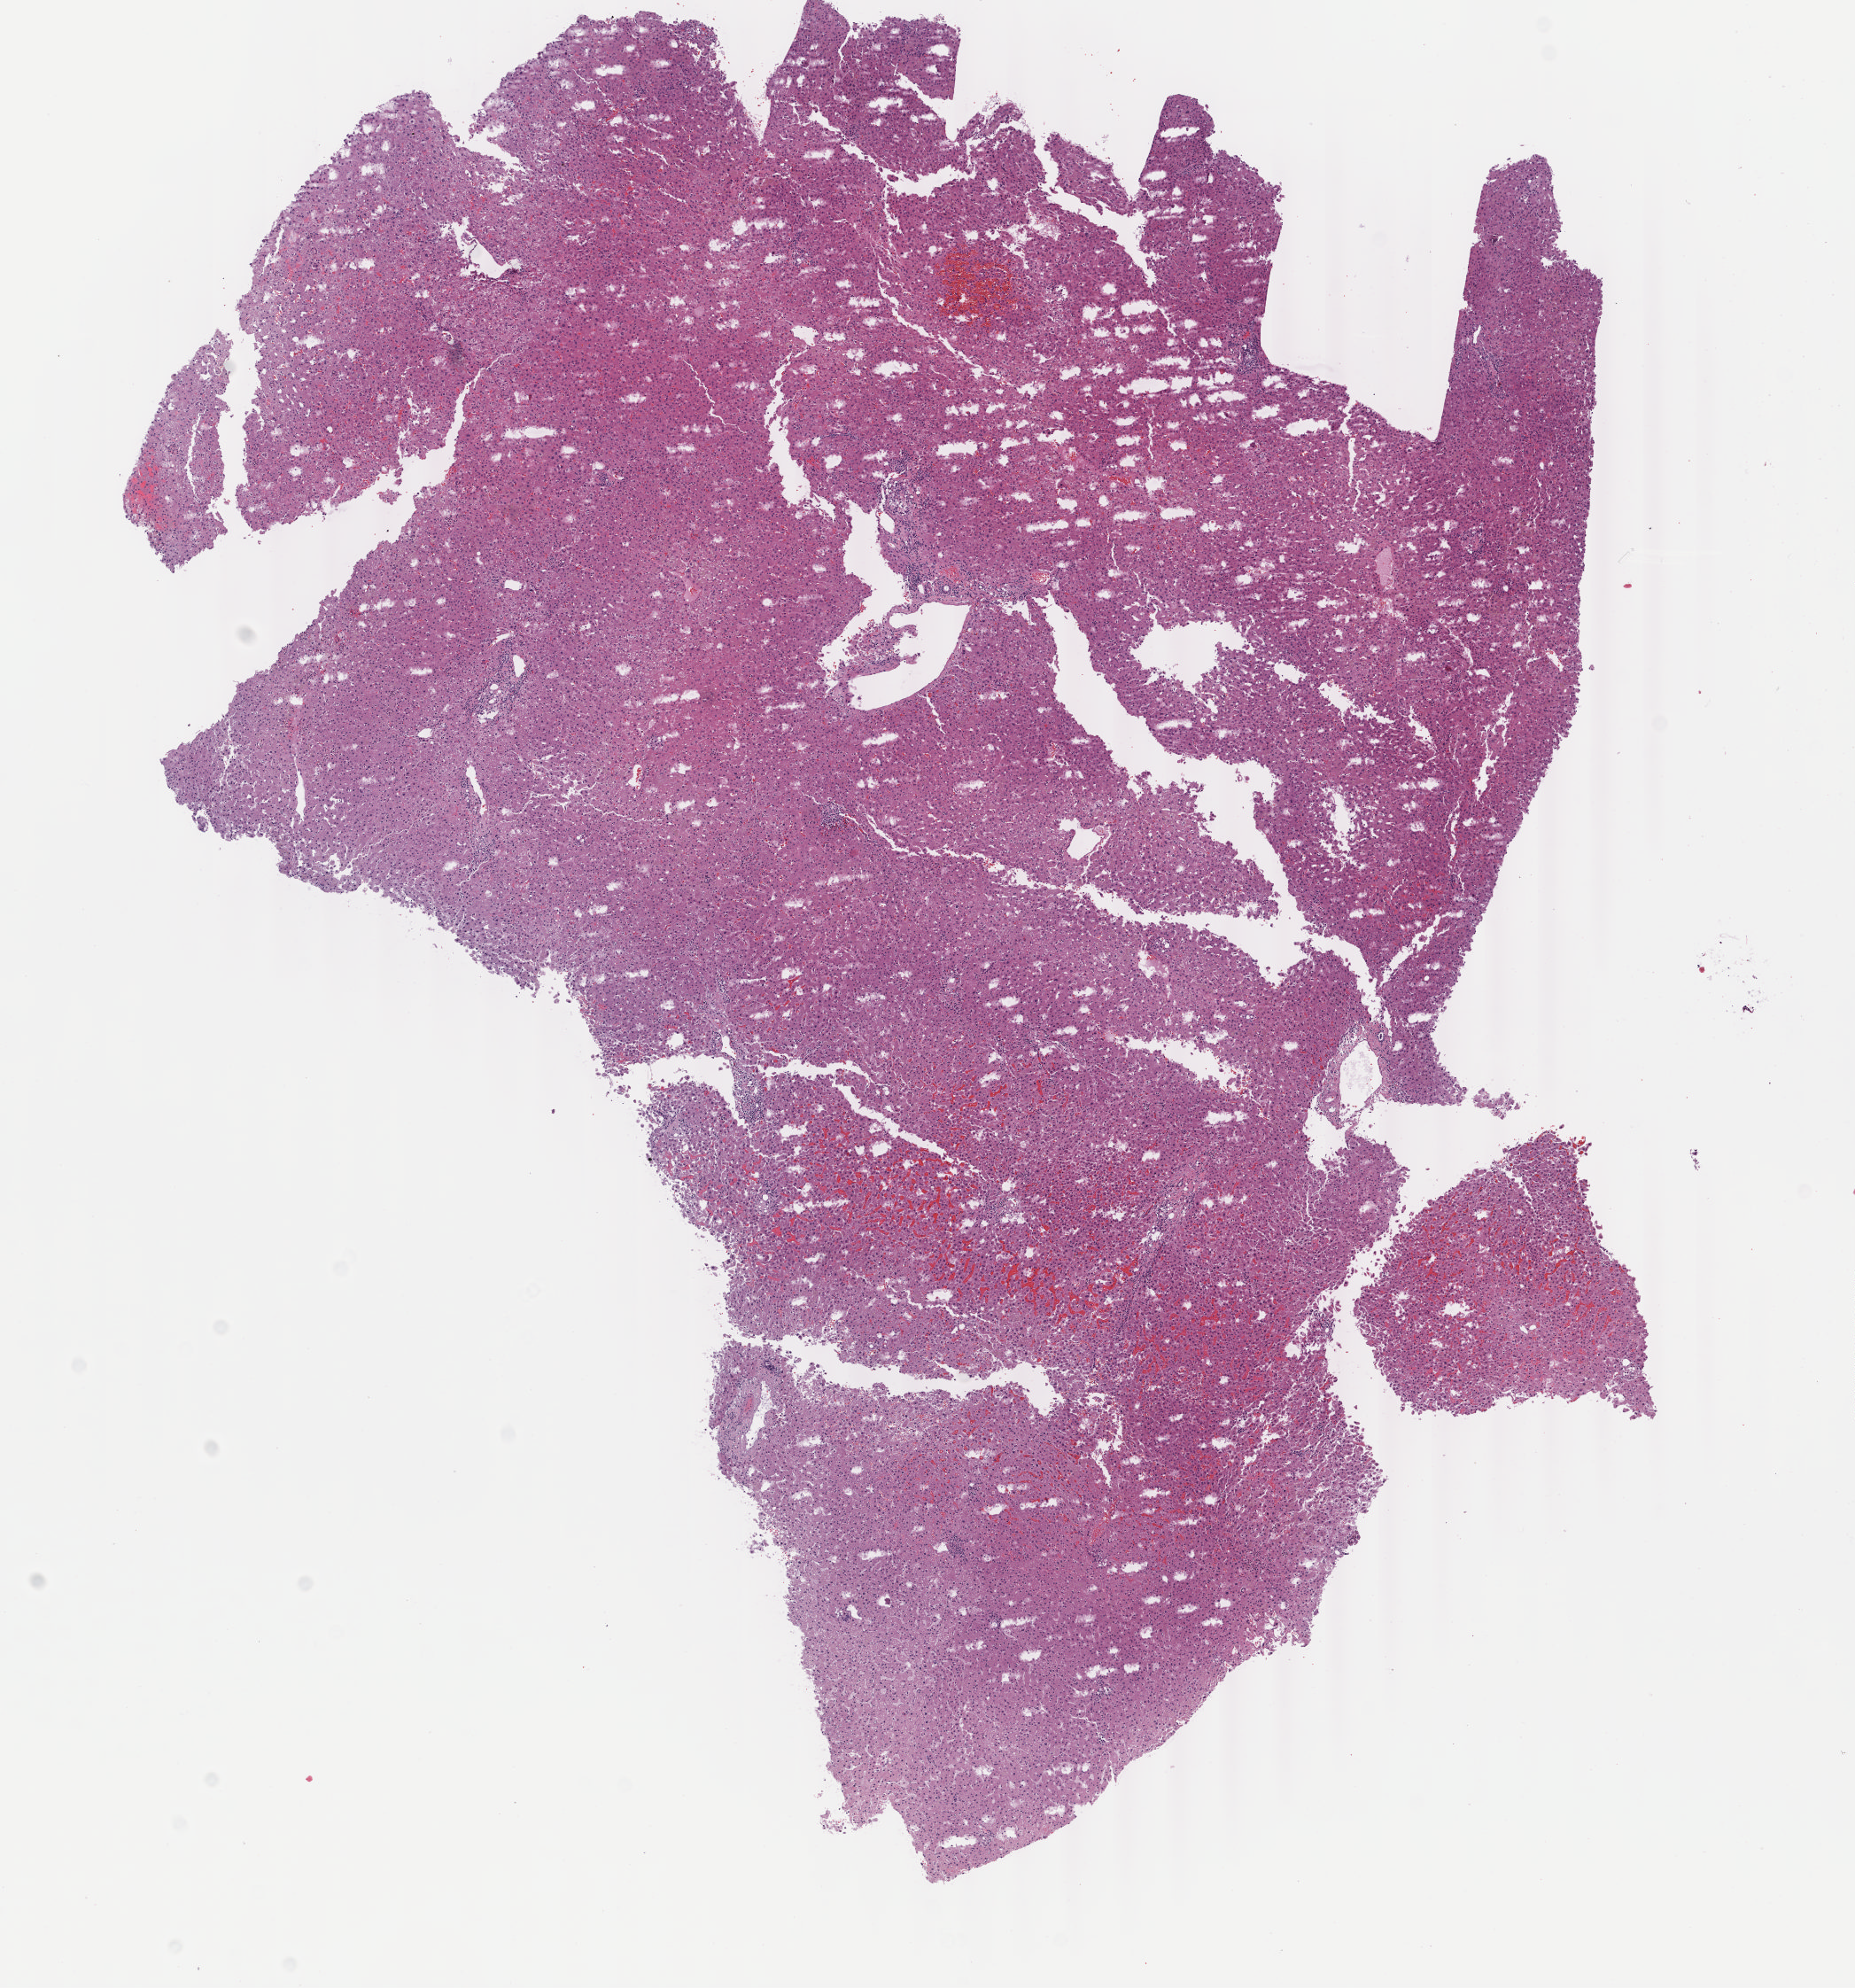
Whole-slide histology image, Hematoxylin and eosin (H&E) stained, shown as a low-resolution overview of the whole scanned area (about 8.3 x 8.9 mm). Formalin-fixed paraffin-embedded (FFPE) diagnostic section. Sample: primary tumour, liver. Female patient; age at initial diagnosis 75 years. Histologic grade: G2 (moderately differentiated).
• histologic diagnosis: Hepatocellular carcinoma, NOS
• AJCC pathologic stage: II (7th edition)